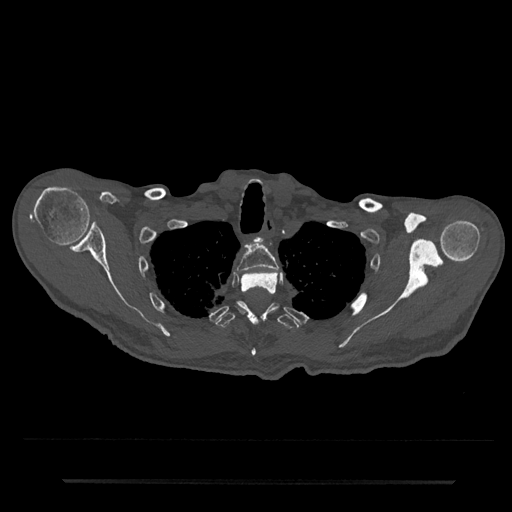
CT including the spine, one axial slice. Slice 653 of 797 in the series (ordered by position). Reconstruction kernel Br40s/3. Bone window (W 1800 / L 400 HU). 0.5 mm slice thickness. 512 × 512 image matrix, field of view 427 × 427 mm. Patient: male, 74 years. Case-level facts recorded for this patient, not image findings: primary cancer: prostate.
Outlined on this slice (semi-automatic segmentation, software-assisted and operator-edited):
- T2 vertebra: bounding box (x1, y1, x2, y2) in pixels: (237, 244, 278, 273)
- T3 vertebra: (240, 272, 278, 356)
- T4 vertebra: (216, 301, 300, 329)